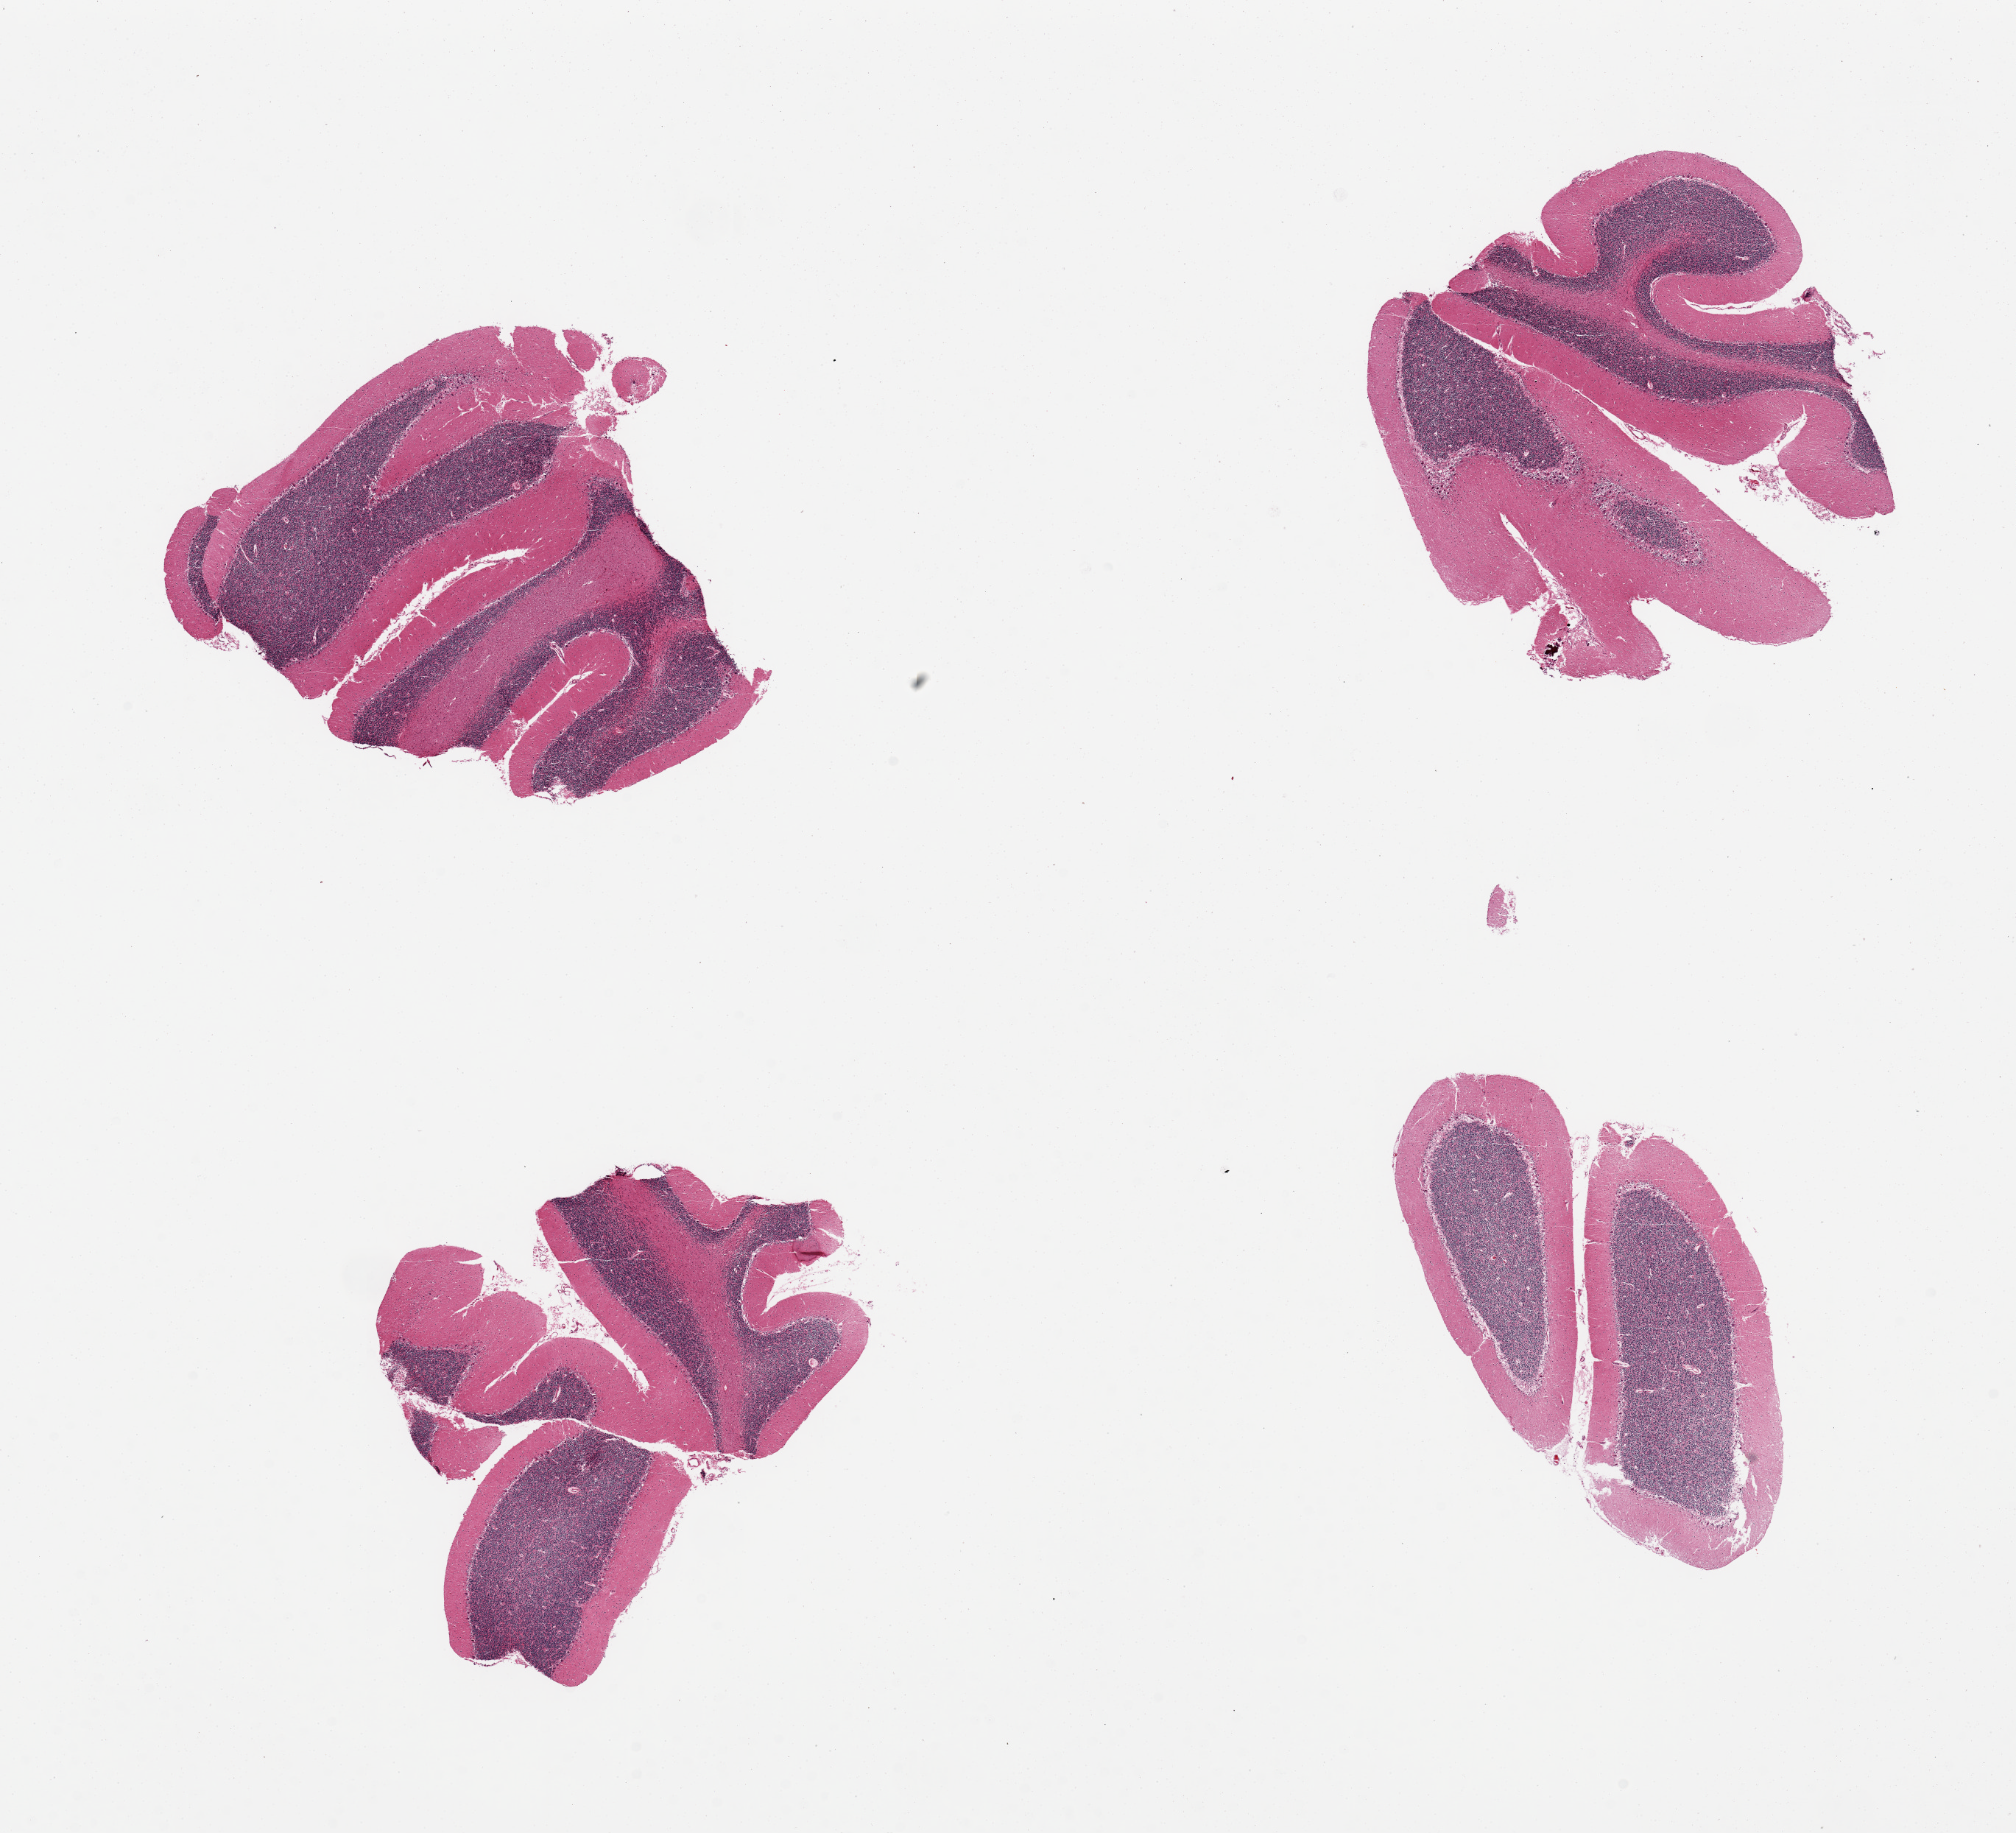
Digitized haematoxylin and eosin-stained section — low-resolution overview of the scanned area, about 21.7 x 19.7 mm, PAXgene-fixed, paraffin-embedded tissue, section of cerebellum (target tissue), tissue donor sample. Female donor.
- pathologist's review note for this sample: 4 pieces, granular layer well-preserved